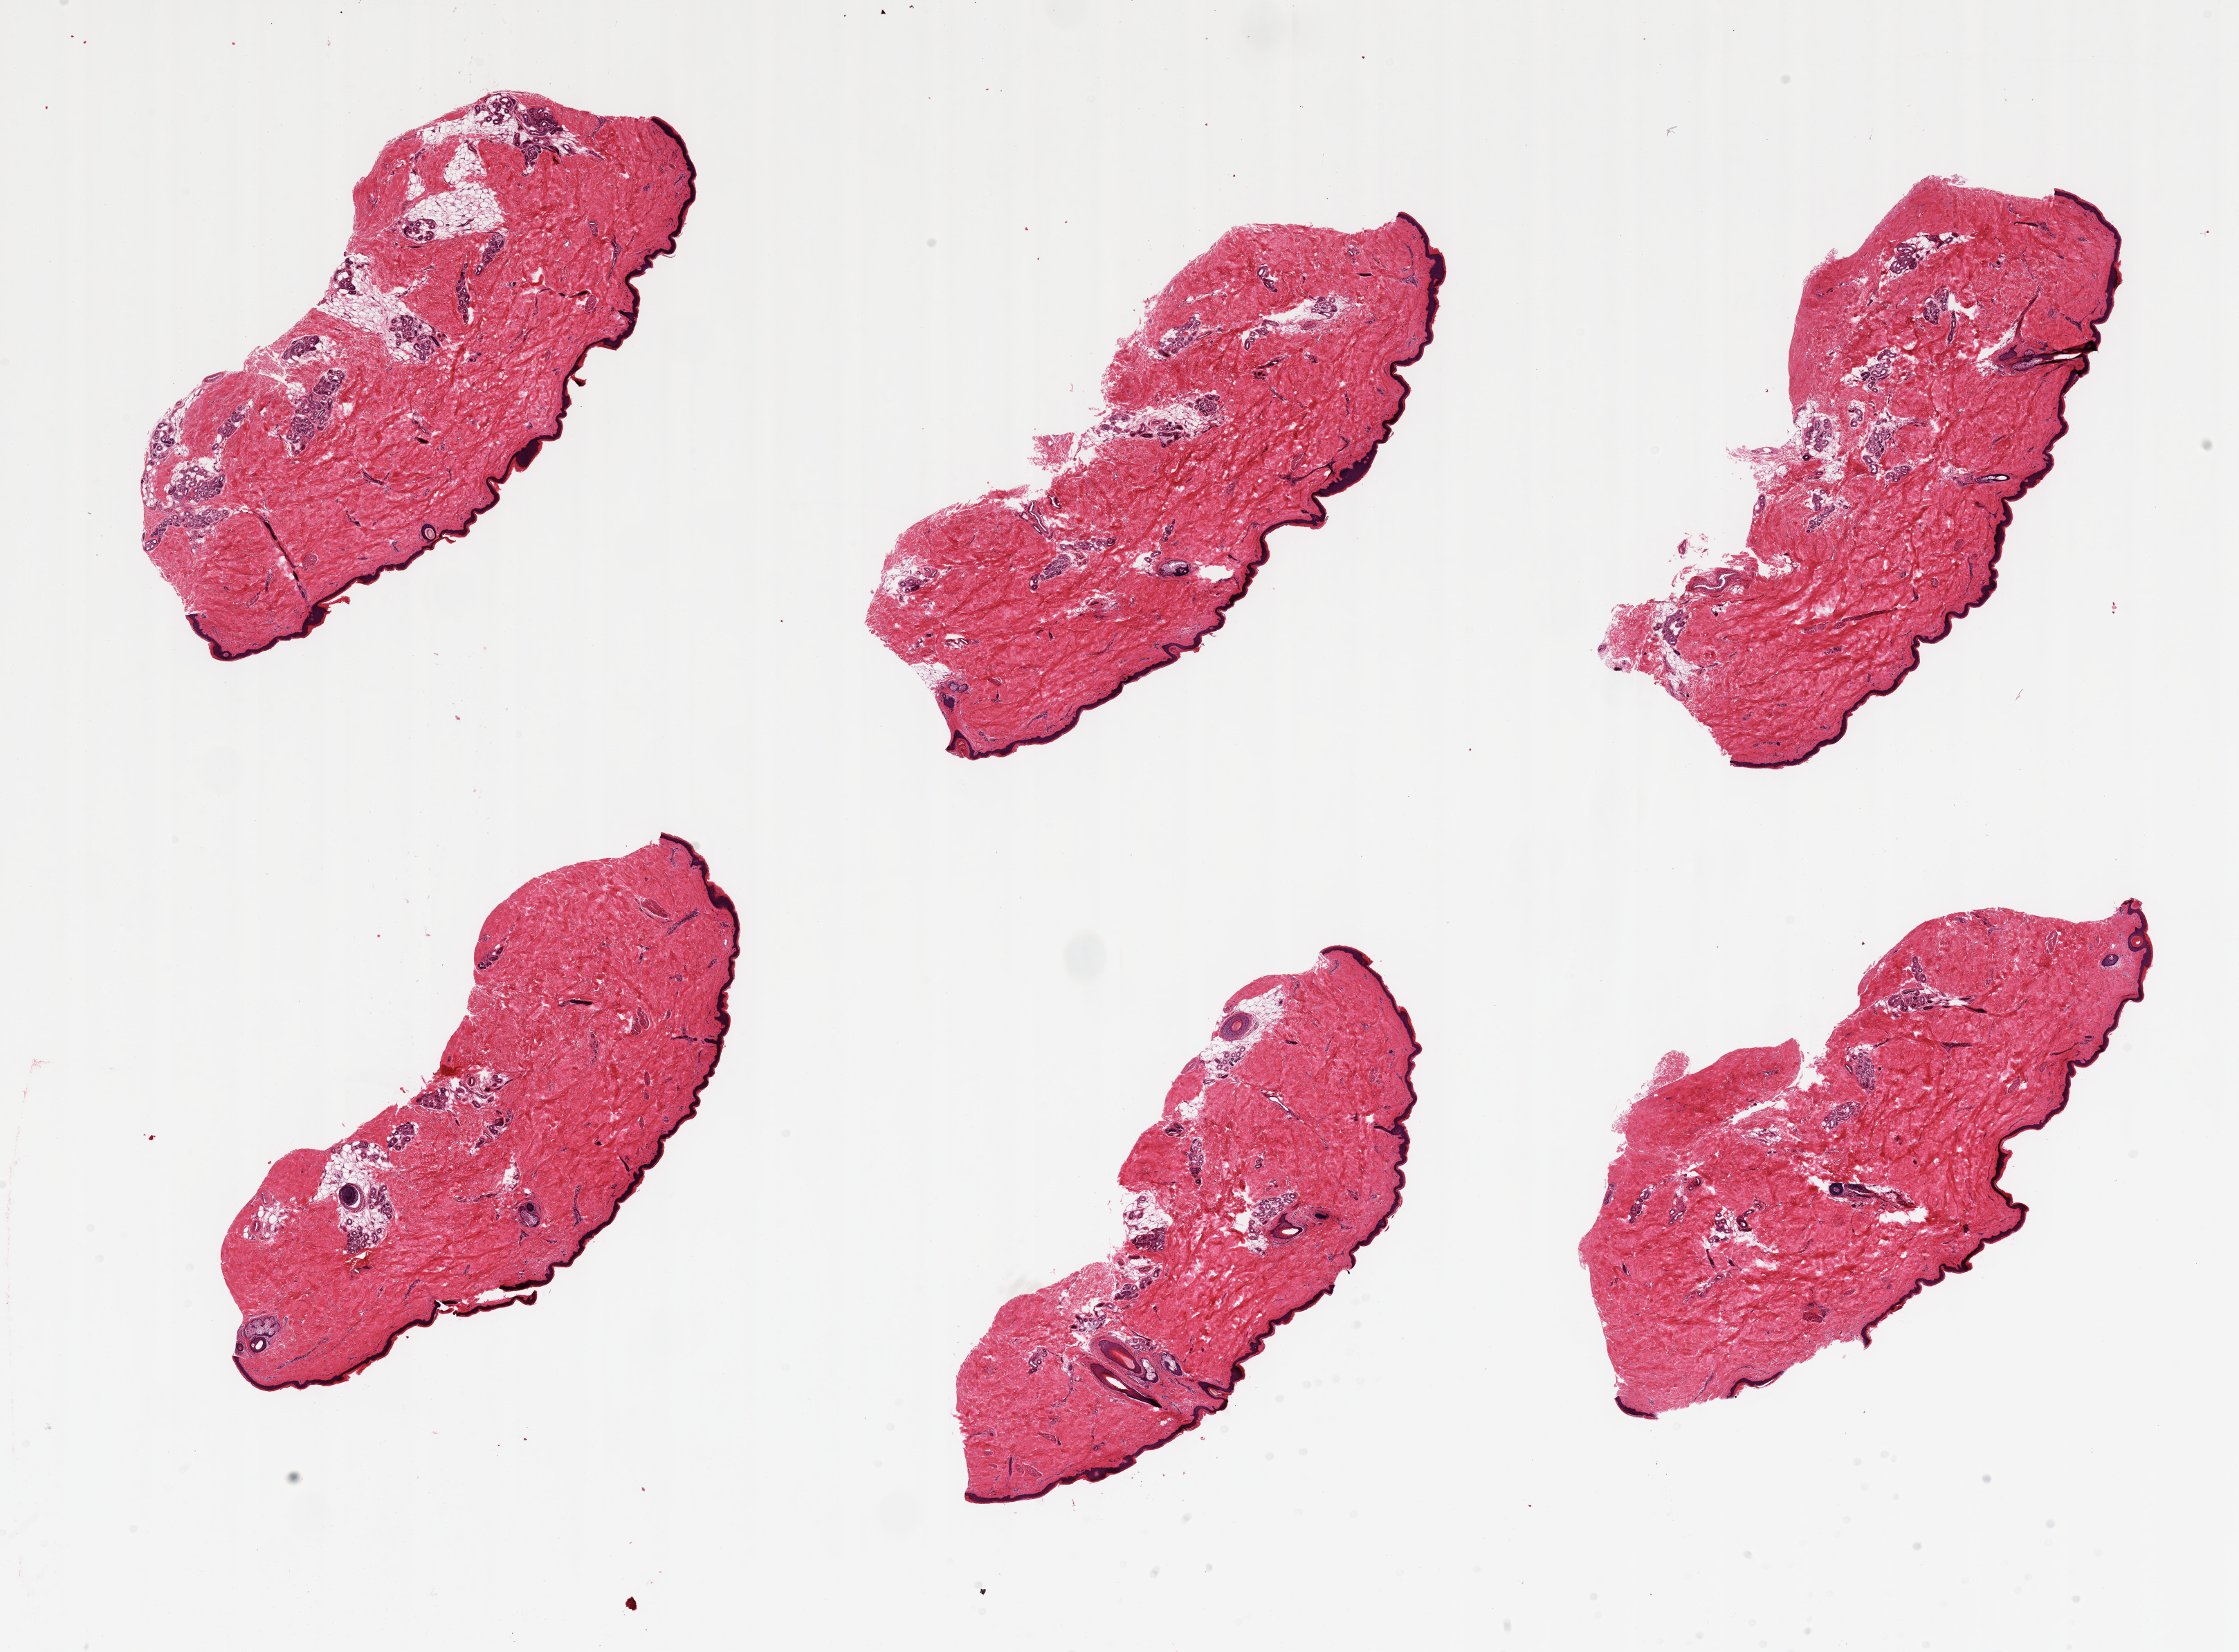
Digitized hematoxylin and eosin (H&E)-stained section, shown as a low-resolution overview of the whole scanned area (about 25.6 x 18.9 mm, acquisition: 20x scan); PAXgene-fixed, paraffin-embedded tissue; target tissue: skin of lower leg; tissue donor sample. Donor sex: male.
Review note (as recorded): 6 pieces; well trimmed; dermal fat 10%.